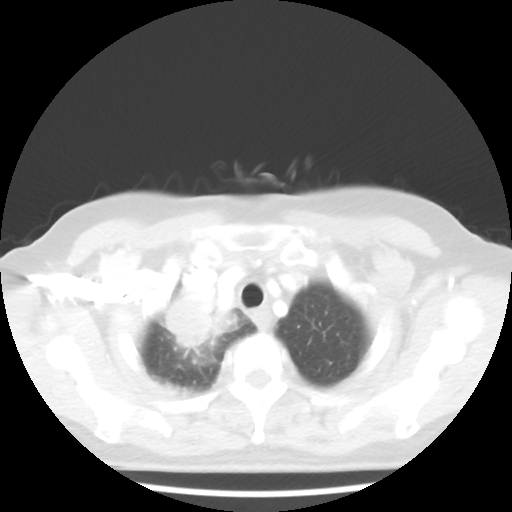
Chest CT, one axial slice. Slice 39 of 44 in the series (ordered by position). Reconstruction kernel STANDARD. Lung window (W 1500 / L -600 HU). 5 mm slice thickness. 512 × 512 image matrix, field of view 316 × 316 mm. Female patient, age 62 years. From the clinical record (not read from this slice): clinical TNM (as recorded): T3 N0 M0.
Outlined on this slice (rectangle marked by the reading radiologist):
- lung tumour (recorded histology: small cell carcinoma): bounding box (x1, y1, x2, y2) in pixels: (164, 283, 223, 359)